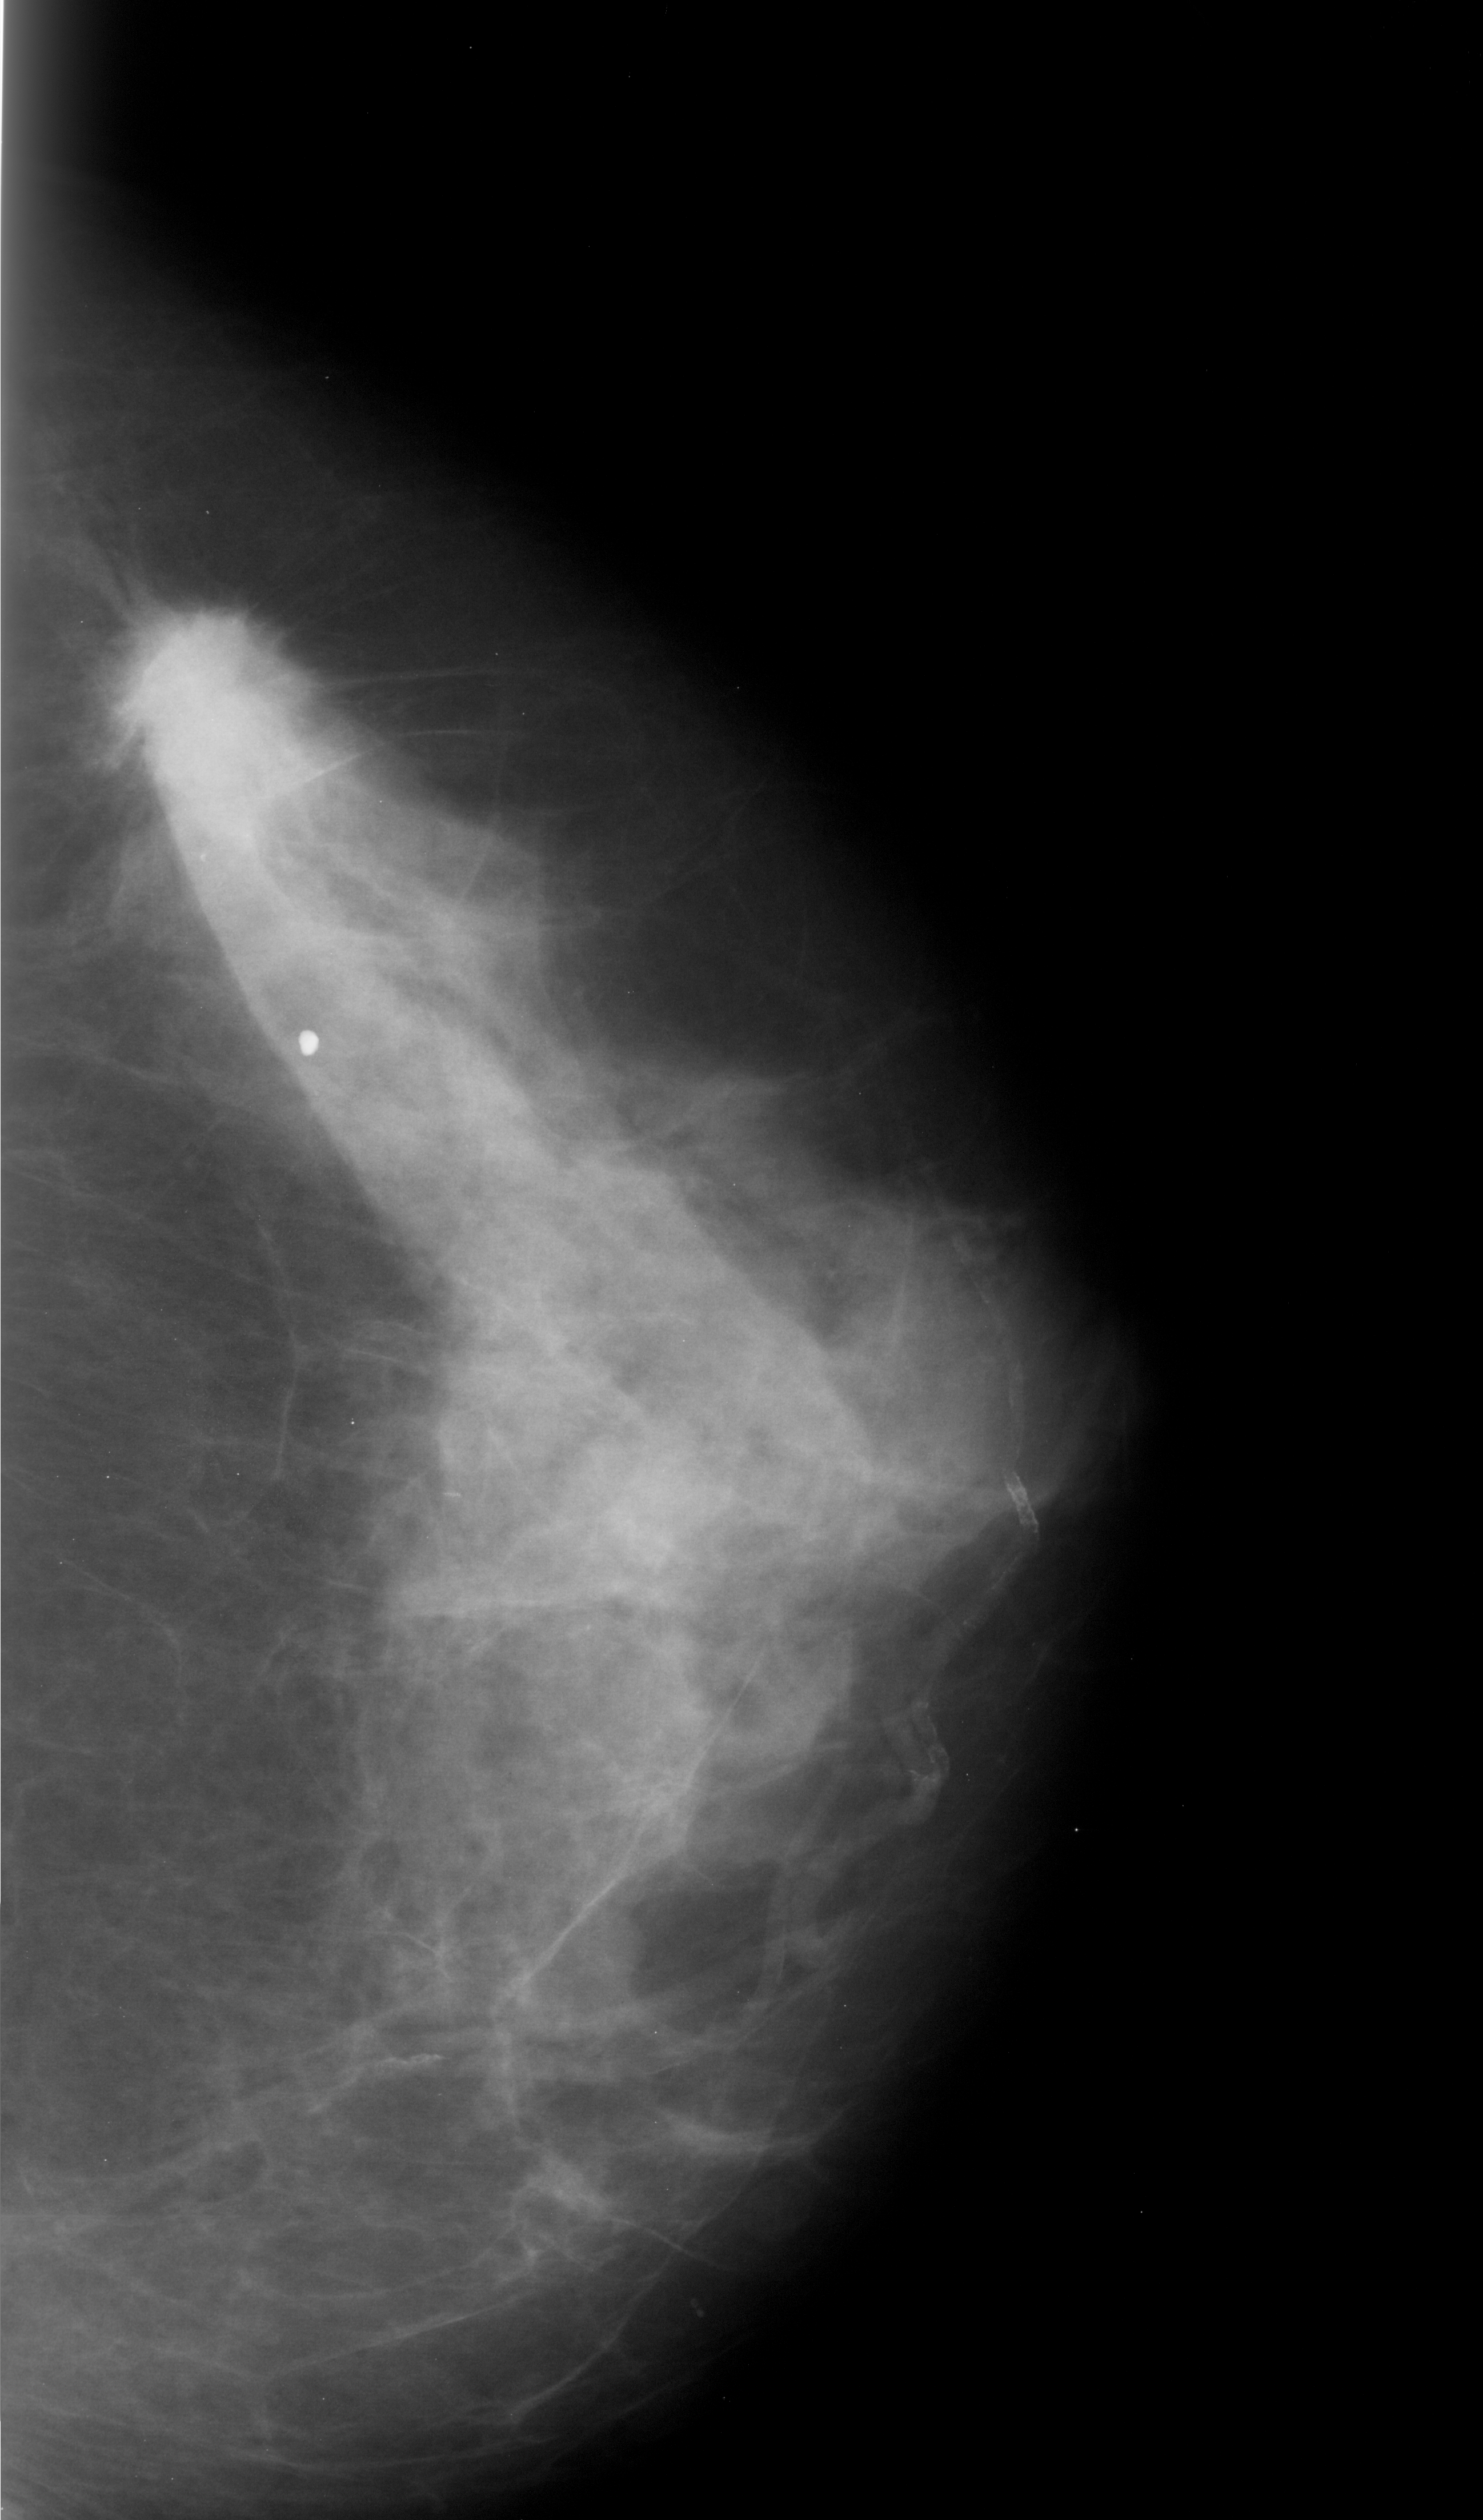
Digitized screen-film mammogram; right breast; craniocaudal (CC) view.
Finding: mass, shape irregular, margins spiculated; BI-RADS assessment category 5; pathology result (as recorded, not read from the image): malignant.